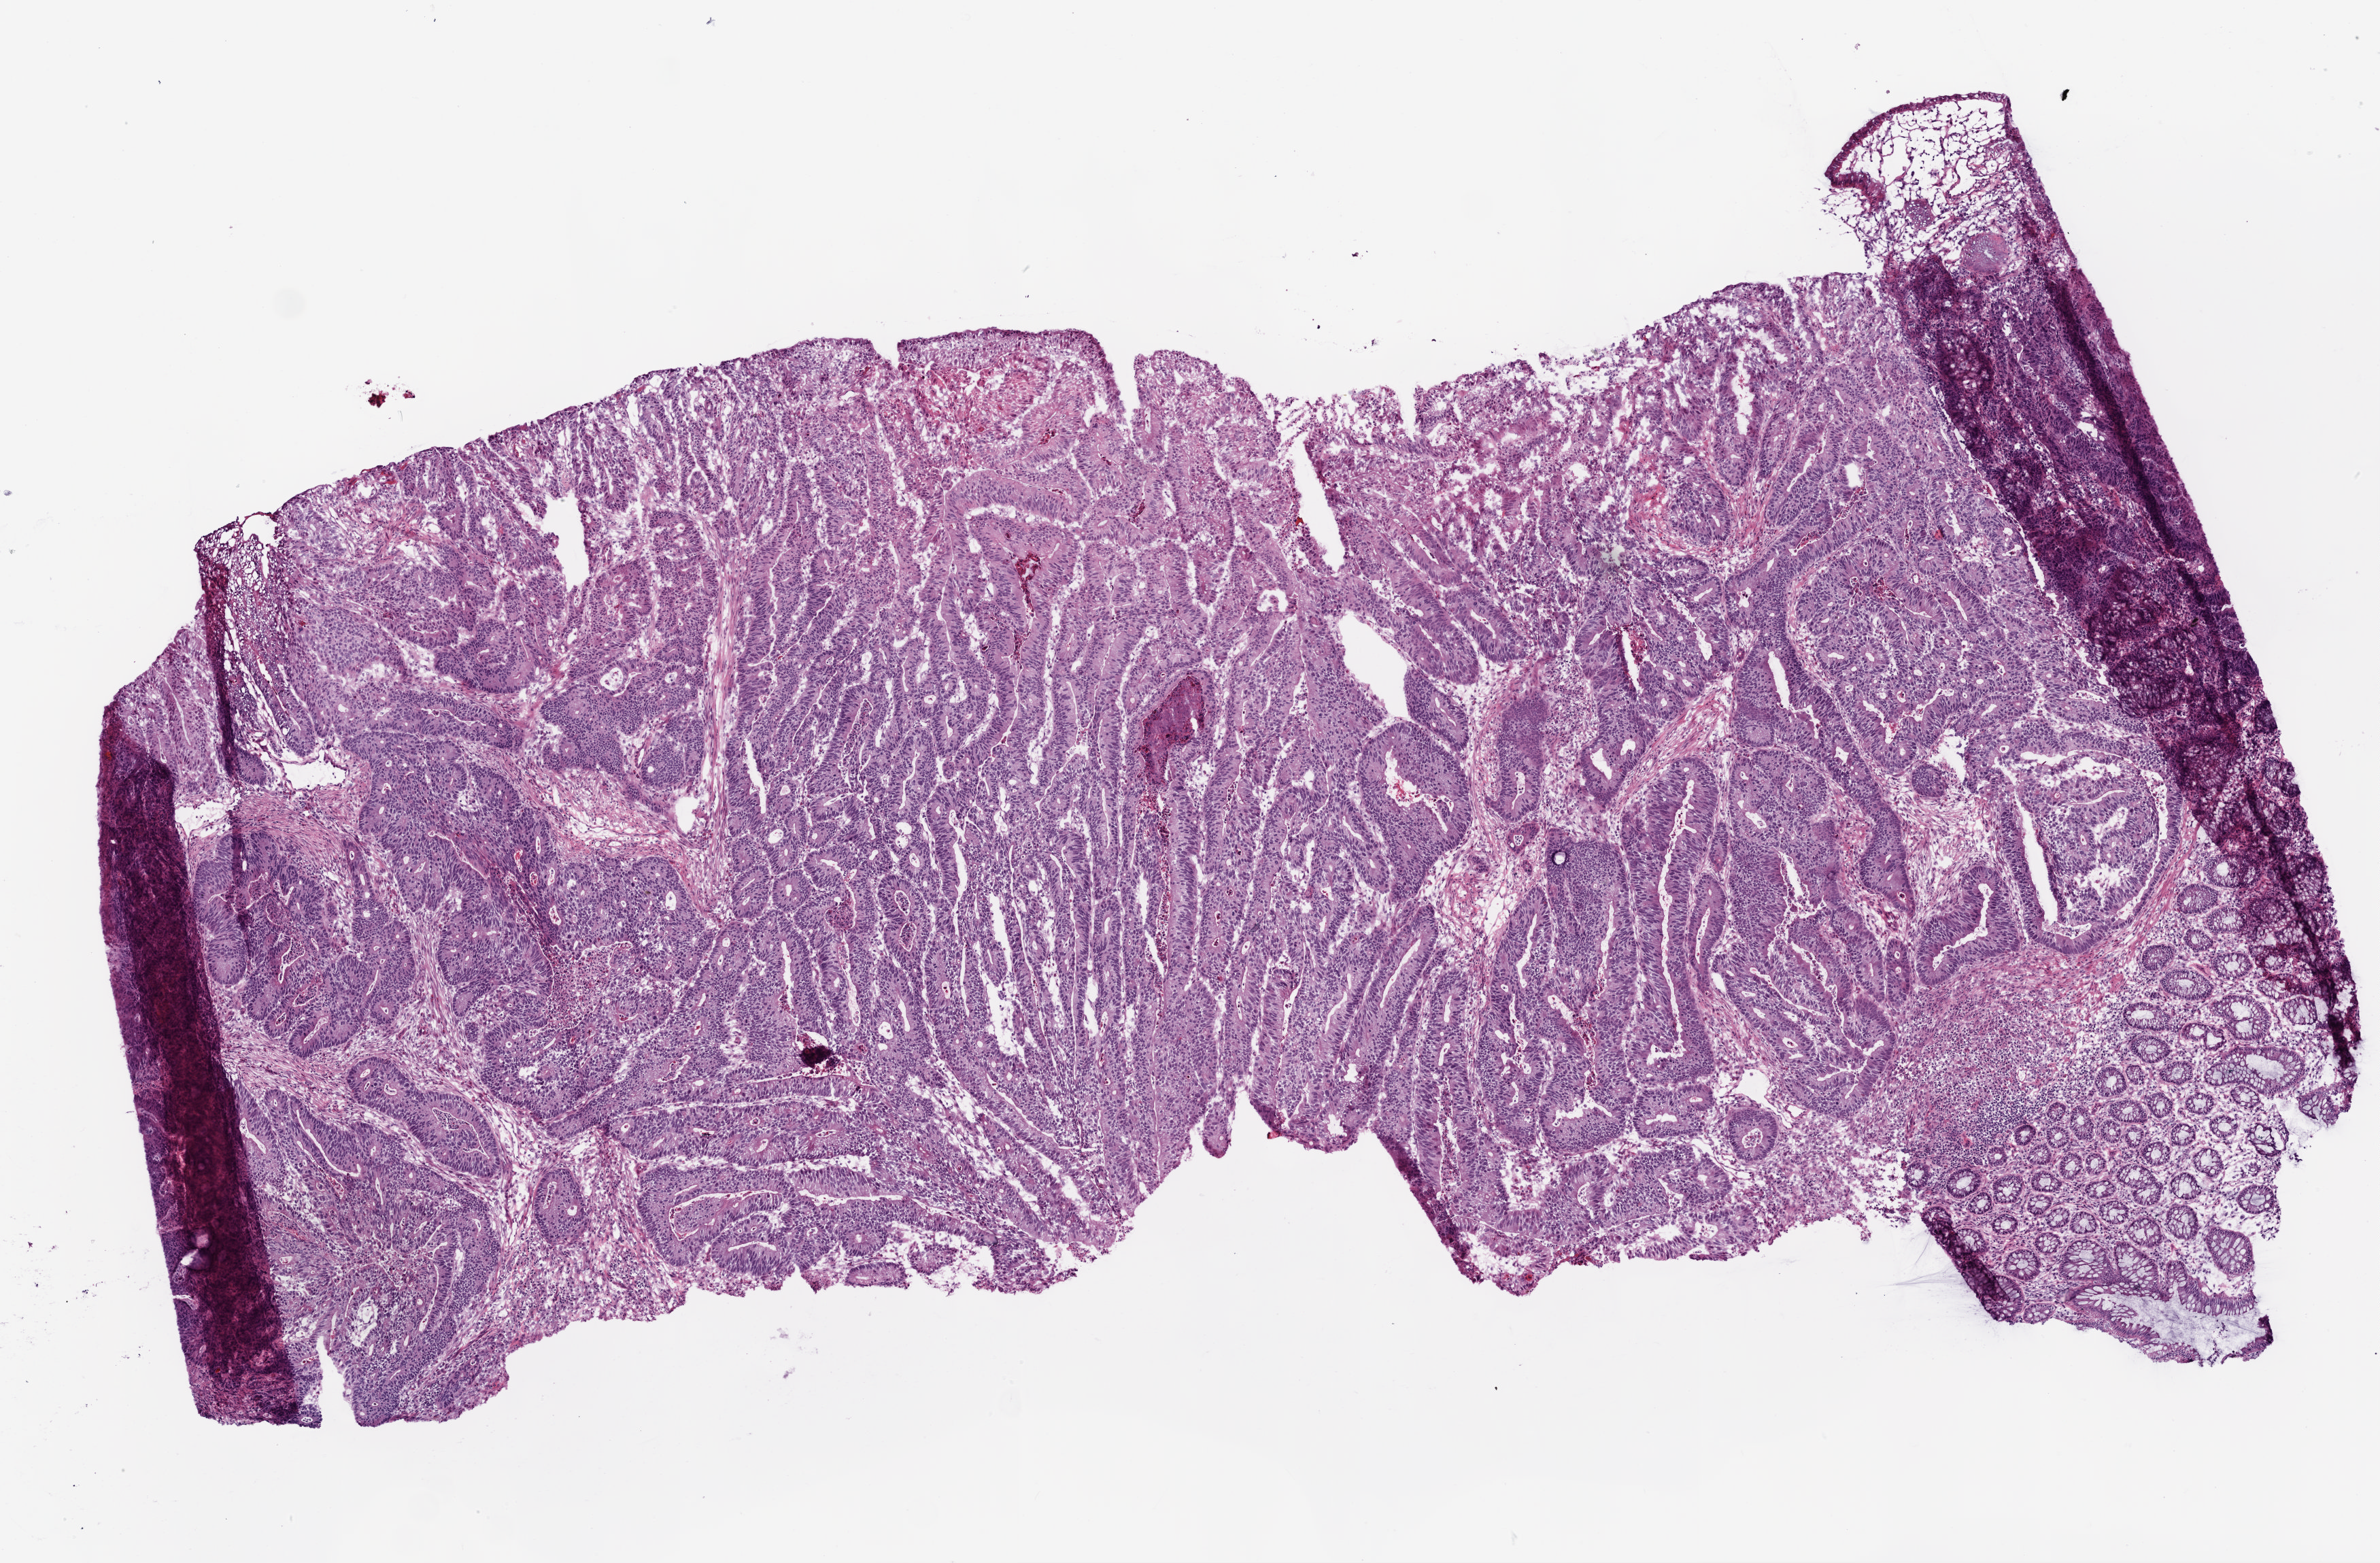
Digitized H&E tissue section (whole slide) — shown as a low-resolution overview of the whole scanned area (about 7.0 x 4.6 mm); frozen section from the bottom of the tissue portion; primary tumour sample from the colon. Female patient; age at initial diagnosis 80 years.
Pathologic diagnosis: Adenocarcinoma, NOS.